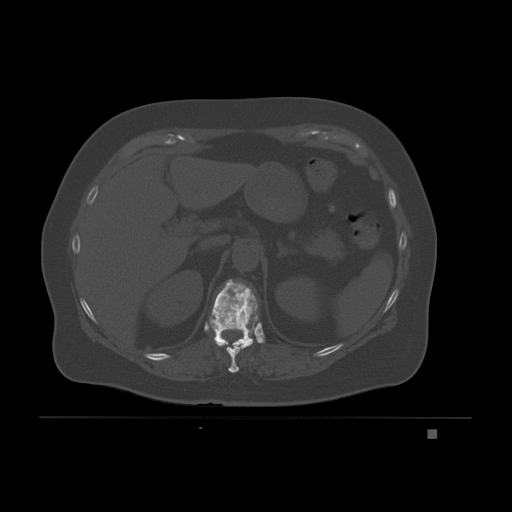
CT including the spine, one axial slice. Position 93 of 221 along the scan axis. Bone window (W 1800 / L 400 HU). 512 × 512 image matrix, field of view 474 × 474 mm. Female patient, age 63 years. From the clinical record (not read from this slice): primary cancer: breast.
Outlined on this slice (semi-automatically segmented with operator editing):
- T10 vertebra: bounding box <216,341,252,373> (left, top, right, bottom; pixels)
- T11 vertebra: <210,279,259,346>